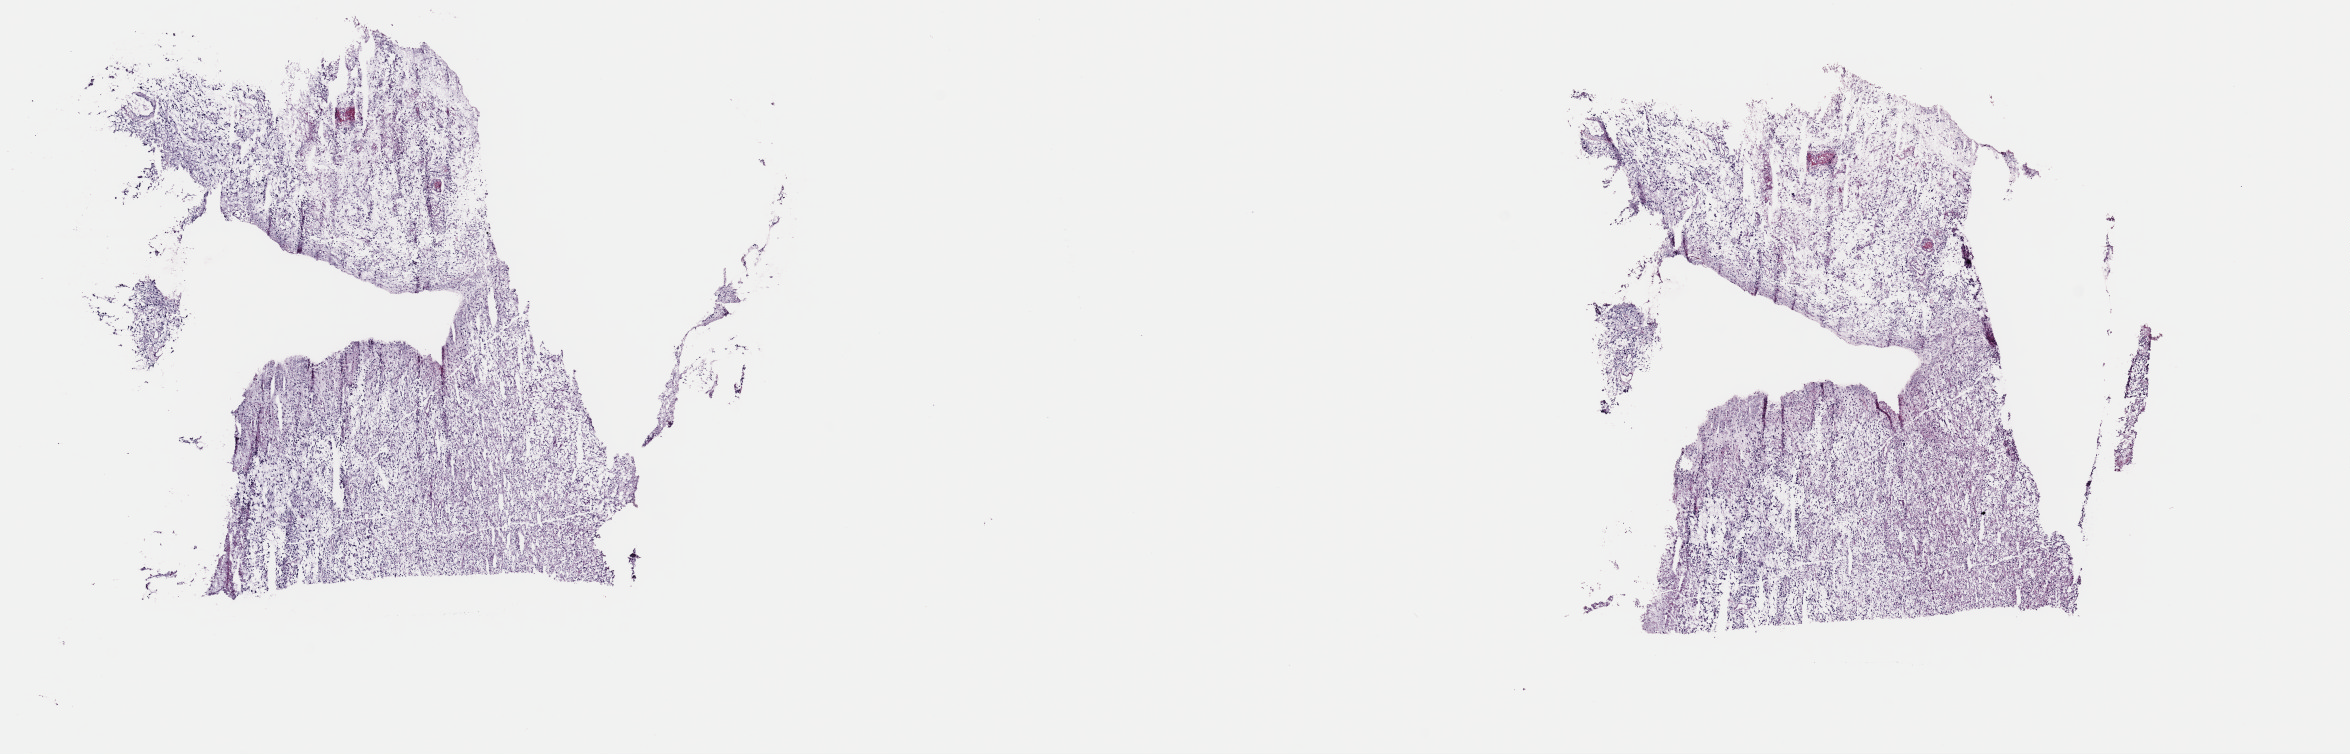
Whole-slide histology image, H&E — a low-resolution overview of the entire scanned area, about 18.6 x 6.0 mm (slide scanned at 40x). Frozen section from the top of the tissue portion. Brain, primary tumour sample. Patient: male, age at initial diagnosis 40 years. Composition of this section per pathologist review: tumour cells 80%, tumour nuclei 85%, normal cells 5%, stromal cells 5%, necrosis 10%. Infiltration values recorded for this section: lymphocyte infiltration 0%, monocyte infiltration 0%, neutrophil infiltration 0%.
• diagnosis: Glioblastoma